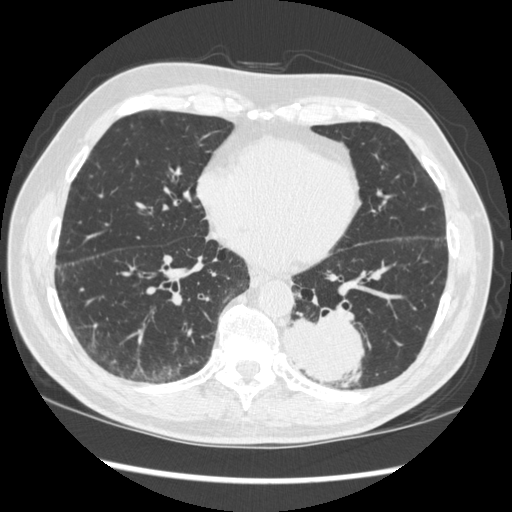
Low-dose screening chest CT, axial slice, baseline screening round, lung window (W 1500 / L -600 HU), 120 kVp, slice 125 of 348 in the series. Male, age 72 years at enrolment. Current smoker at enrolment.
- Expert reader's lesion annotation, bounding box (x1, y1, x2, y2) in pixels: (272, 297, 376, 386).
- The screening reader recorded 2 non-calcified nodules or masses ≥4 mm on this exam; which of them this box marks is not recorded.
- Official screen result: positive, change unspecified: nodule(s) >= 4 mm or enlarging nodule(s), mass(es), or other non-specific abnormalities suspicious for lung cancer.
- Participant outcome: lung cancer diagnosed 37 days after this screen — squamous cell carcinoma, NOS, left lower lobe, stage IIIA (AJCC 6th edition), 60 mm at pathology.